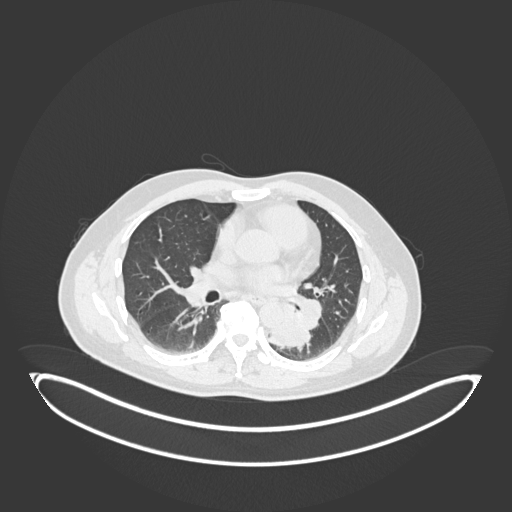
Chest CT, one axial slice; slice 101 of 258 in the series (ordered by position); lung window (W 1500 / L -600 HU); 1 mm slice thickness; 512 × 512 image matrix, field of view 500 × 500 mm. Male patient, age 54 years. From the clinical record (not read from this slice): clinical TNM (as recorded): T3 N0 M0.
Outlined on this slice (bounding box drawn by a radiologist):
- lung tumour (recorded histology: squamous cell carcinoma): bounding box (x1, y1, x2, y2) in pixels: (266, 315, 314, 357)